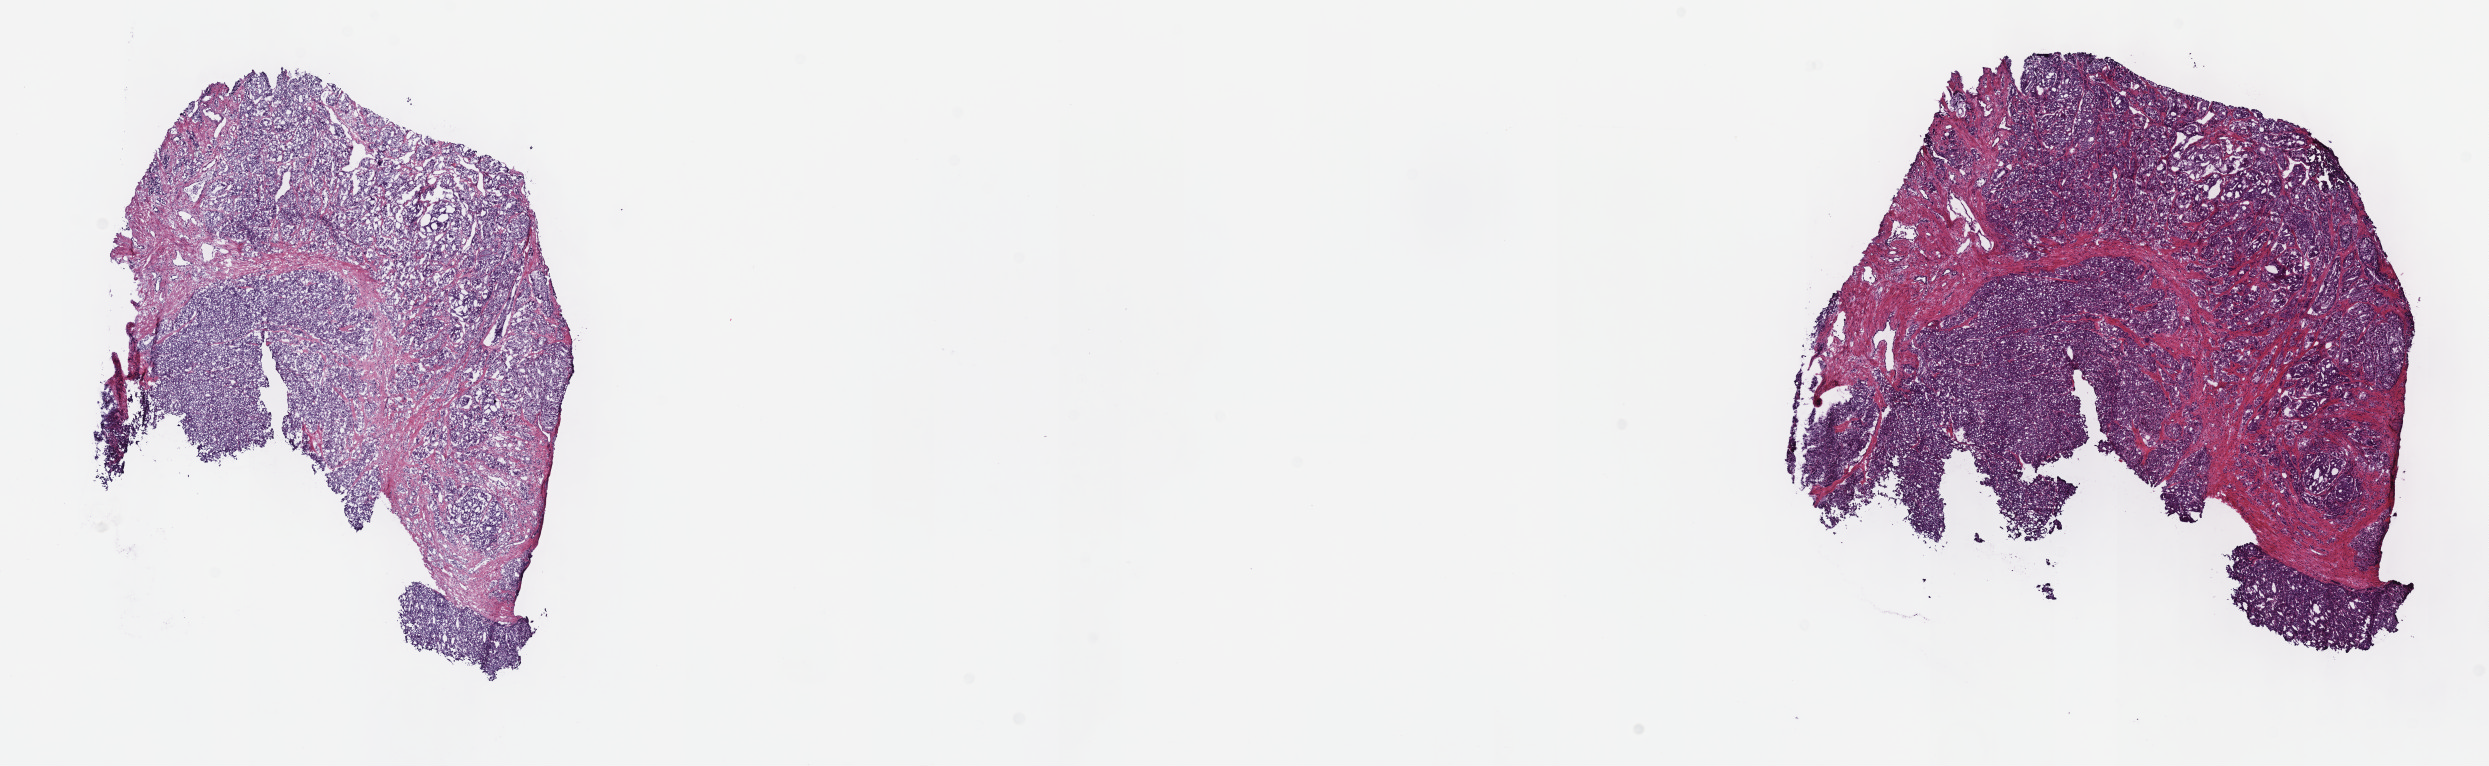
Whole-slide histology image, H&E — low-resolution overview of the scanned area, about 20.1 x 6.2 mm, frozen section from the top of the tissue portion, prostate, primary tumour sample. Patient: male, age at initial diagnosis 69 years. Gleason score: 9 (4+5). Slide review estimates, as recorded: tumour cells 70%, tumour nuclei 80%, normal cells 5%, stromal cells 25%, necrosis 0%. Inflammatory infiltration, as recorded: lymphocyte infiltration 0%, monocyte infiltration 0%, neutrophil infiltration 0%.
Lymph nodes positive (case pathology): 0 of 3 examined. Pathologic diagnosis: Adenocarcinoma, NOS.